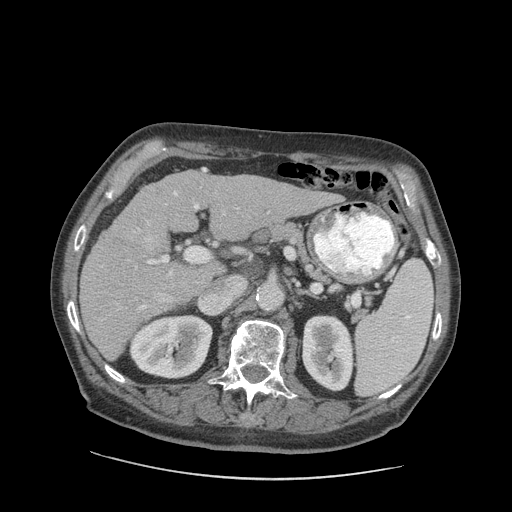
Contrast-enhanced abdominal CT (liver protocol), one axial slice; slice 49 of 89 in the series (ordered by position); 140 kVp; soft-tissue window (W 400 / L 40 HU); 2.5 mm slice thickness; 512 × 512 image matrix, field of view 420 × 420 mm. Case-level facts recorded for this patient, not image findings: diagnosis: hepatocellular carcinoma (patient treated with transarterial chemoembolisation; whether this scan precedes or follows treatment is not stated here); TNM stage (as recorded): Stage-I; Child-Pugh class: A; tumour differentiation: moderately differentiated; tumour nodularity: uninodular.
Annotated regions visible in this slice (semi-automatically segmented with operator editing):
- liver parenchyma outside the tumour (the mass and vessels are separate outlines, so this box may not span the whole liver): box from (x=79, y=168) to (x=336, y=360) px
- mass: (x=141, y=230)–(x=168, y=253)
- liver vessels: (x=100, y=169)–(x=269, y=321)